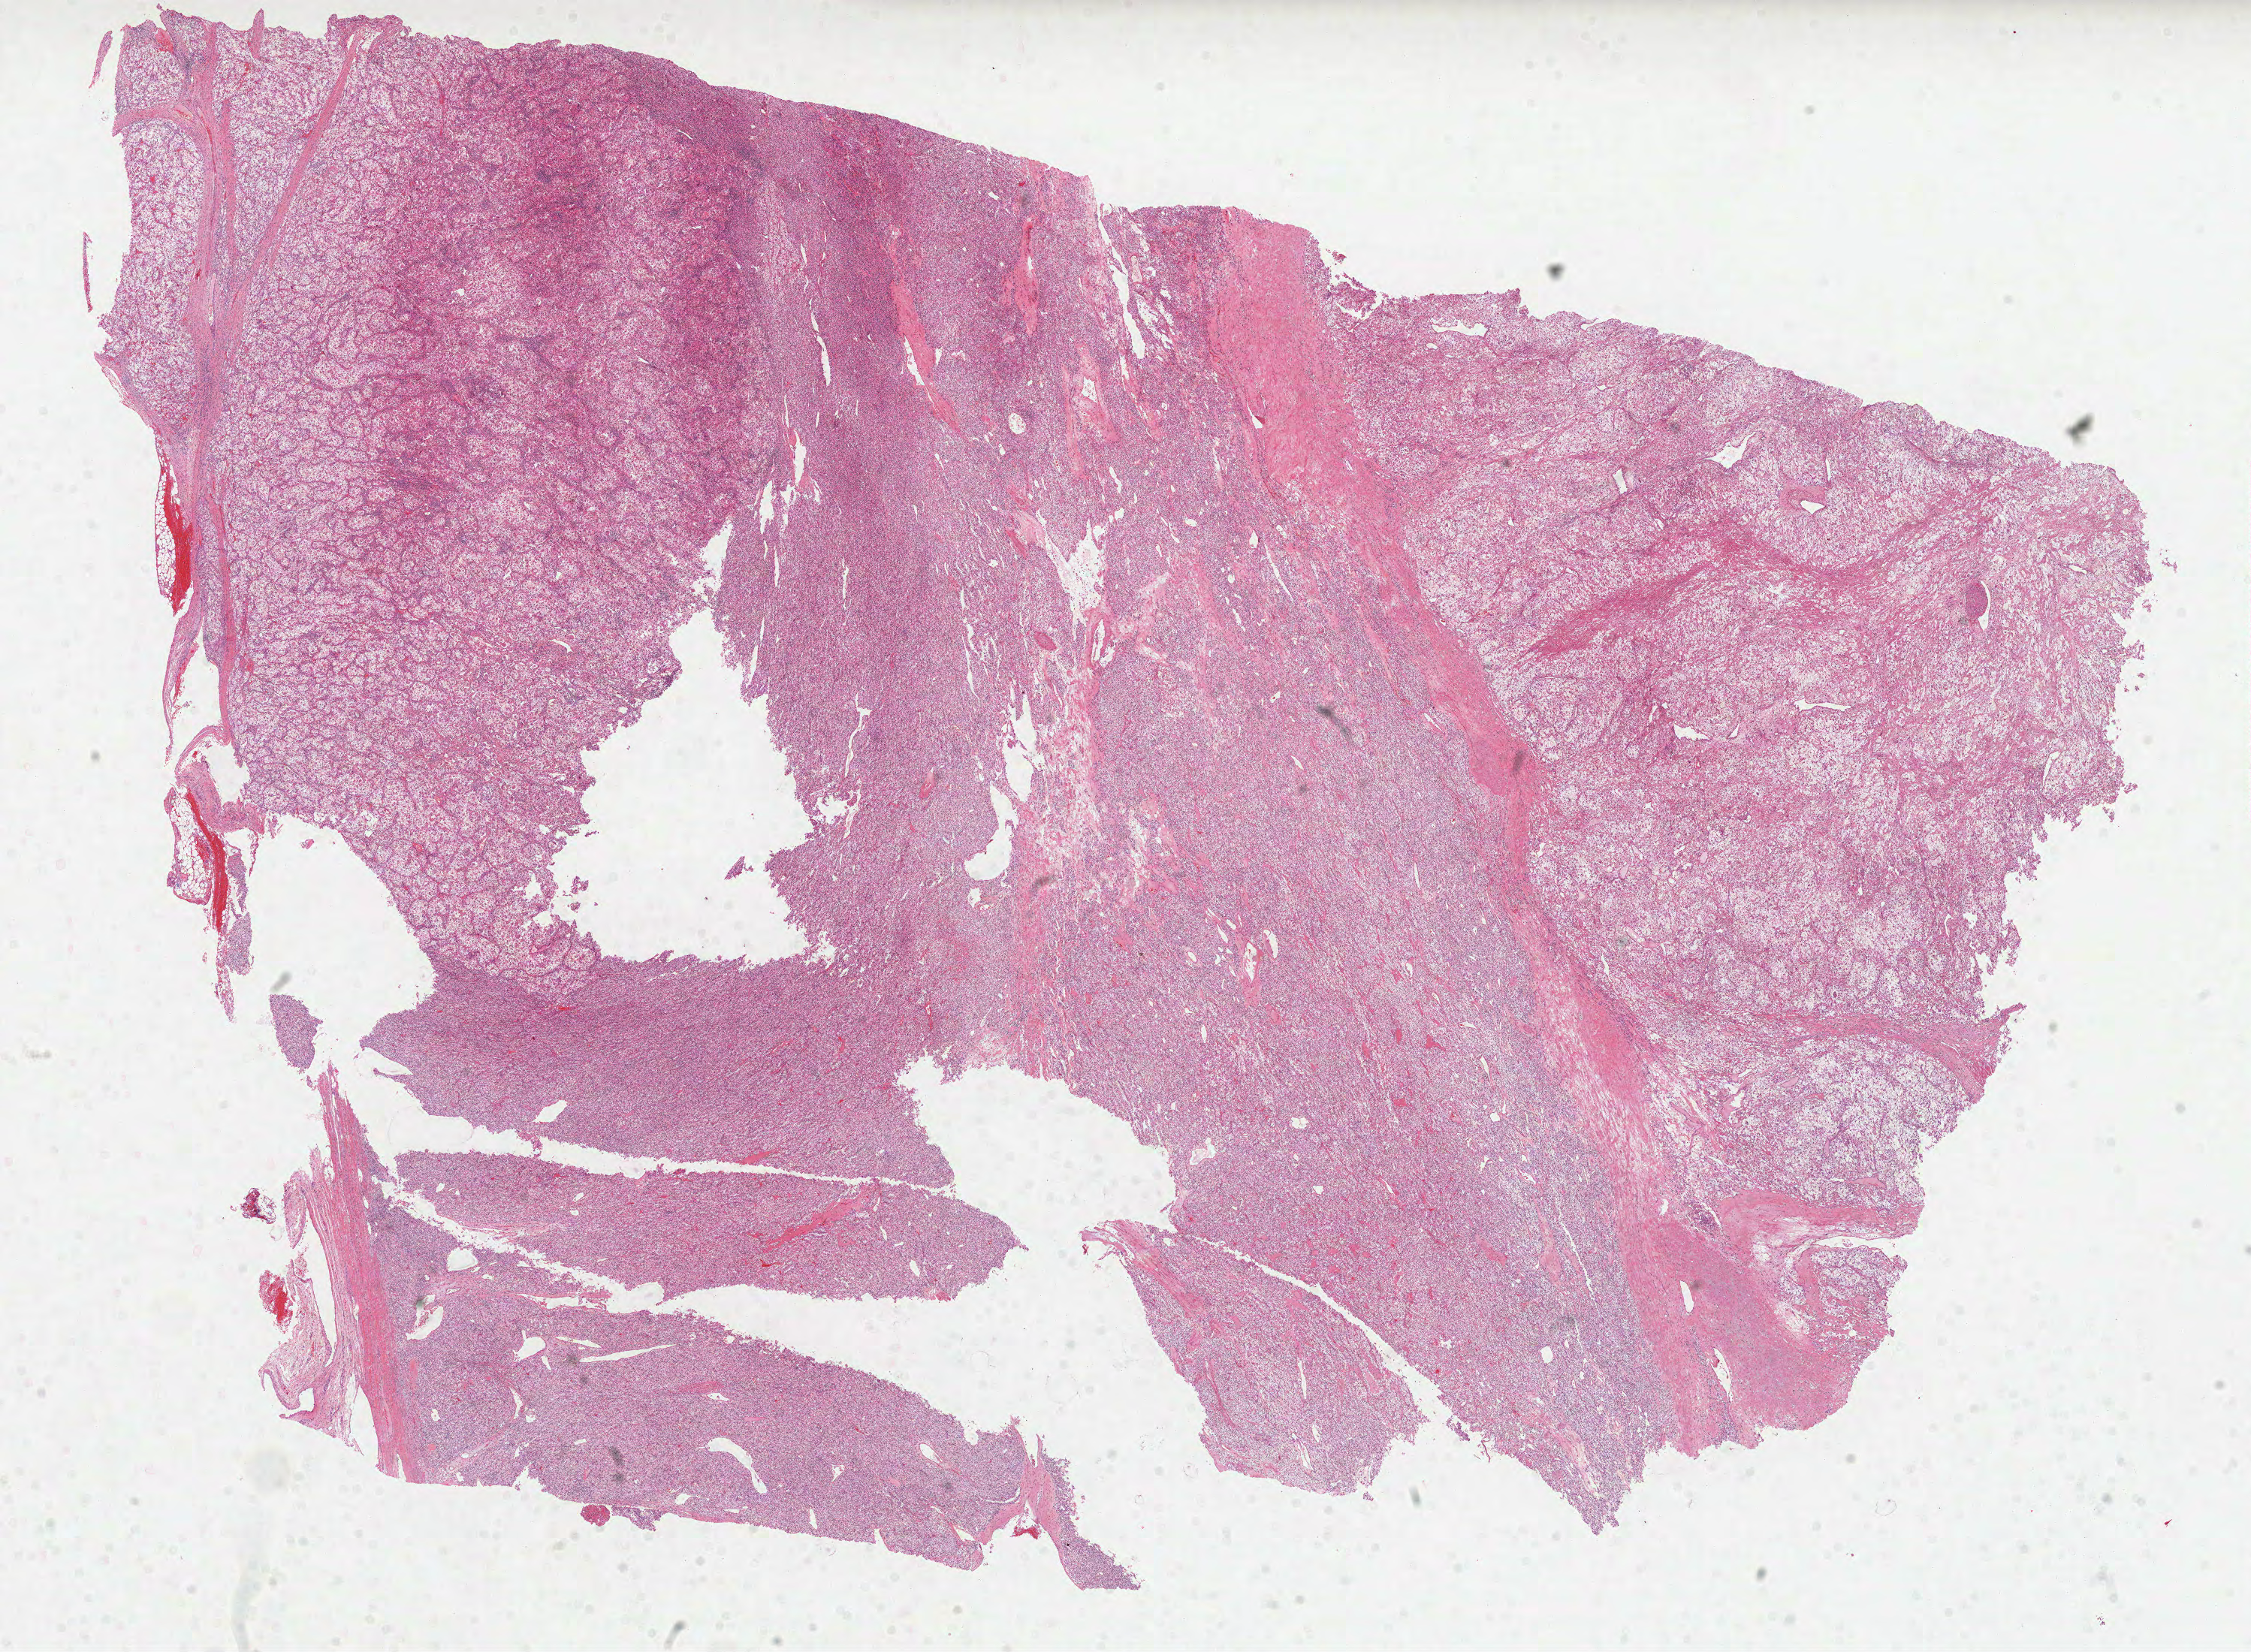
Whole-slide histology image, H&E-stained — low-resolution overview of the scanned area, about 24.2 x 17.7 mm (acquisition: 40x scan). FFPE section. Primary tumour sample from the kidney. Patient: male, age at initial diagnosis 54 years. Histologic grade: G3 (poorly differentiated).
- laterality: left
- AJCC pathologic stage: III
- TNM: T3b NX M0
- pathologic diagnosis: Clear cell adenocarcinoma, NOS